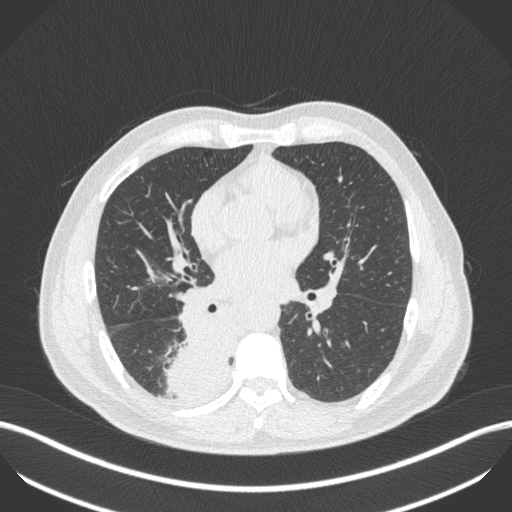
Chest CT, one axial slice. Position 236 of 451 along the scan axis. Lung window (W 1500 / L -600 HU). 512 × 512 image matrix. Male patient, age 61 years. From the clinical record (not read from this slice): clinical TNM (as recorded): T1 N0 M0; histopathological grade: G3.
Structures marked on this image (bounding box drawn by a radiologist):
- lung tumour (recorded histology: small cell carcinoma): bounding box <163,314,242,398> (left, top, right, bottom; pixels)